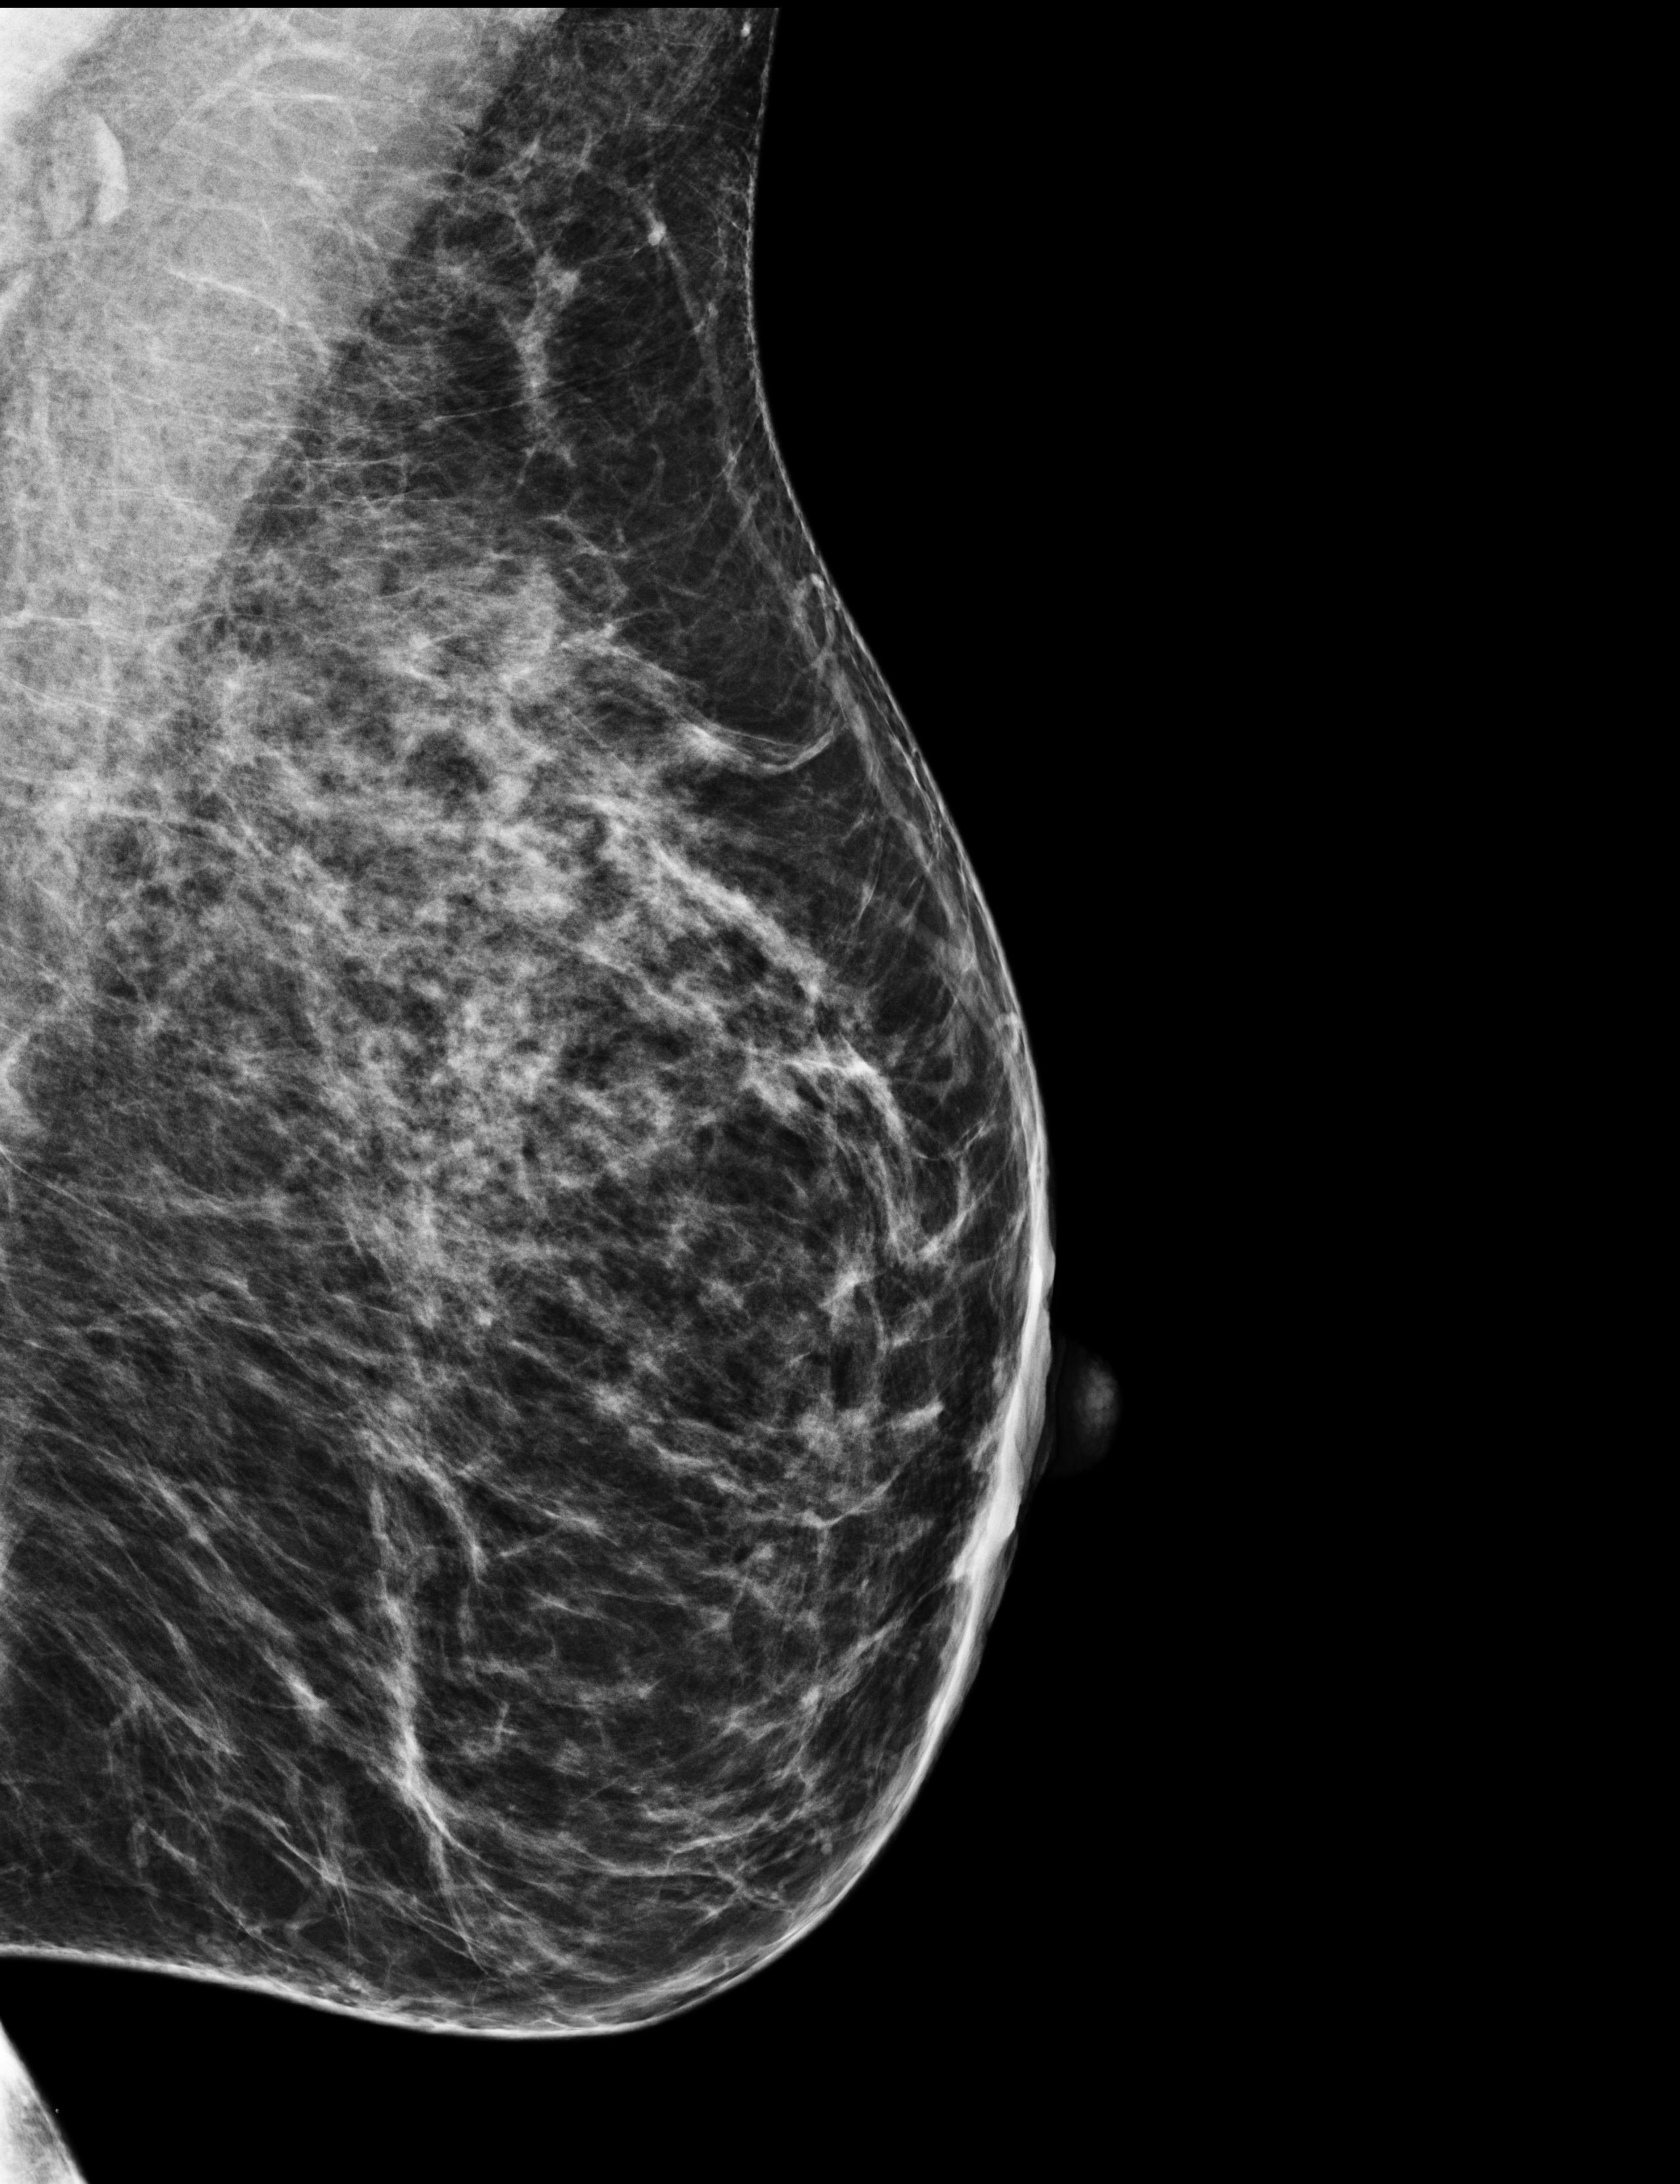
Full-field digital mammogram (FFDM), left breast, MLO view, annual screening mammography examination. Patient: female, 62 years.
- BI-RADS breast density category at the screening exam (both breasts, scale 1–4): 3
- final BI-RADS assessment for this screening round (tomosynthesis exam, both breasts): category 1
- recall: no recall after this screen